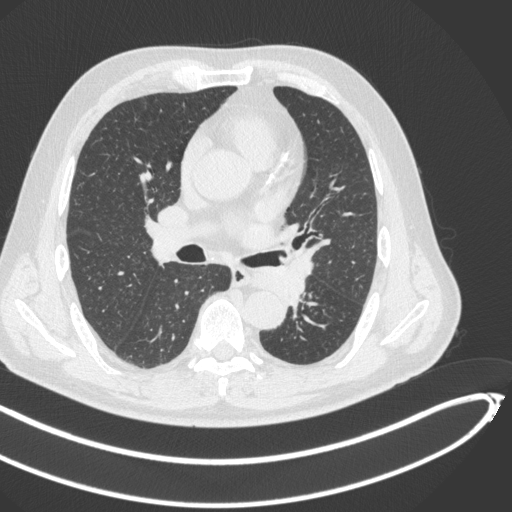
Chest CT, one axial slice. Slice 259 of 466 in the series (ordered by position). Reconstruction kernel B31f. 120 kVp. Lung window (W 1500 / L -600 HU). 512 × 512 image matrix, field of view 400 × 400 mm. Male patient, age 64 years. From the clinical record (not read from this slice): clinical TNM (as recorded): T1c N0 M0.
Outlined on this slice (rectangle marked by the reading radiologist):
- lung tumour (recorded histology: squamous cell carcinoma): box from (x=251, y=250) to (x=317, y=300) px